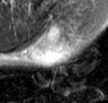
MRI of an extremity soft-tissue mass, one axial slice. Position 31 of 42 along the scan axis. T2-weighted fat-saturated. MR volume resampled by the dataset authors to the PET/CT grid (not the native acquisition matrix). 3.27 mm slice thickness. 108 × 103 image matrix, field of view 105 × 101 mm. Male patient. From the clinical record (not read from this slice): histological type: leiomyosarcoma; grade: intermediate; site of the primary tumour: left pelvis.
Annotated regions visible in this slice (expert contour drawn on MRI and transferred to this co-registered scan by the dataset authors):
- gross tumour volume (mass): bounding box [x1, y1, x2, y2] px = [30, 21, 79, 66]